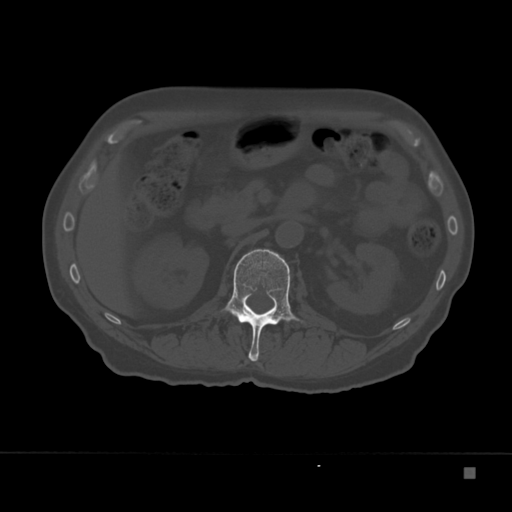
CT including the spine, one axial slice. Position 110 of 332 along the scan axis. Bone window (W 1800 / L 400 HU). 1.5 mm slice thickness. 512 × 512 image matrix, field of view 389 × 389 mm. Male patient, age 72 years. From the clinical record (not read from this slice): primary cancer: skeletal.
Outlined on this slice (semi-automatically segmented with operator editing):
- L1 vertebra: bounding box (x1, y1, x2, y2) in pixels: (221, 249, 303, 362)